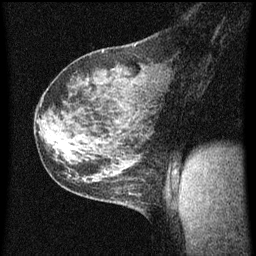
Breast MRI (dynamic contrast-enhanced), one sagittal slice; dynamic contrast-enhanced series, image 2 of 3 at this slice position (ordered by acquisition); 1.5 T; TE 4.2 ms, TR 8 ms; 2 mm slice thickness; 256 × 256 image matrix, field of view 180 × 180 mm. Patient: female, 35 years.
Annotated regions visible in this slice (semi-automatically segmented with operator editing):
- analysis volume of interest (the breast-tissue region the enhancement analysis was run in; not a lesion): bounding box [x1, y1, x2, y2] px = [106, 182, 149, 215]
- tumour enhancement mask (voxels above the 70 % enhancement threshold inside the analysis volume of interest): [128, 190, 141, 195]